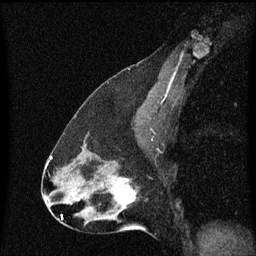
Breast MRI (dynamic contrast-enhanced), one sagittal slice; dynamic contrast-enhanced series, image 2 of 3 at this slice position (ordered by acquisition); 1.5 T; TE 4.2 ms, TR 8.4 ms; 2 mm slice thickness; 256 × 256 image matrix, field of view 200 × 200 mm. Female patient, age 47 years.
Annotated regions visible in this slice (semi-automatically segmented with operator editing):
- analysis volume of interest (the breast-tissue region the enhancement analysis was run in; not a lesion): bounding box (x1, y1, x2, y2) in pixels: (100, 172, 148, 219)
- tumour enhancement mask (voxels above the 70 % enhancement threshold inside the analysis volume of interest): (113, 178, 137, 213)